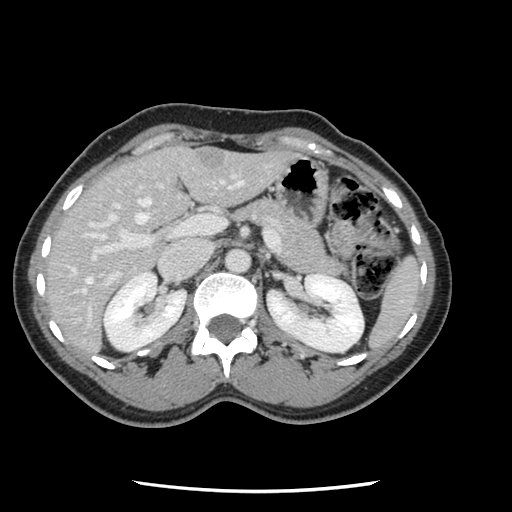
Contrast-enhanced abdominal CT, one axial slice. Position 66 of 134 along the scan axis. Intravenous contrast given. Soft-tissue window (W 400 / L 40 HU). 2.5 mm slice thickness. 512 × 512 image matrix, field of view 330 × 330 mm. Female patient, age 43 years. From the clinical record (not read from this slice): diagnosis: colorectal cancer liver metastases, imaged before liver resection; multiple liver metastases: yes; largest metastasis: 3.4 cm.
Annotated regions visible in this slice (outlined manually by an expert reader):
- hepatic veins: bounding box <73,181,243,293> (left, top, right, bottom; pixels)
- liver: <46,146,292,353>
- planned liver remnant (the part of the liver to remain after resection): <46,150,185,305>
- portal vein (with intrahepatic branches): <71,175,276,326>
- liver metastasis: <196,154,225,169>